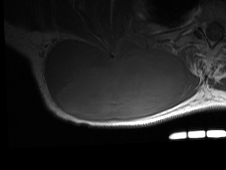
MRI of an extremity soft-tissue mass, one axial slice. Slice 41 of 81 in the series (ordered by position). MR volume resampled by the dataset authors to the PET/CT grid (not the native acquisition matrix). 3.27 mm slice thickness. 226 × 170 image matrix, field of view 221 × 166 mm. Male patient. From the clinical record (not read from this slice): histological type: pleiomorphic spindle cell undifferentiated; grade: high; site of the primary tumour: right parascapusular.
Annotated regions visible in this slice (expert contour drawn on MRI and transferred to this co-registered scan by the dataset authors):
- gross tumour volume including surrounding oedema: box from (x=42, y=36) to (x=198, y=123) px
- gross tumour volume (mass): (x=42, y=40)–(x=184, y=121)